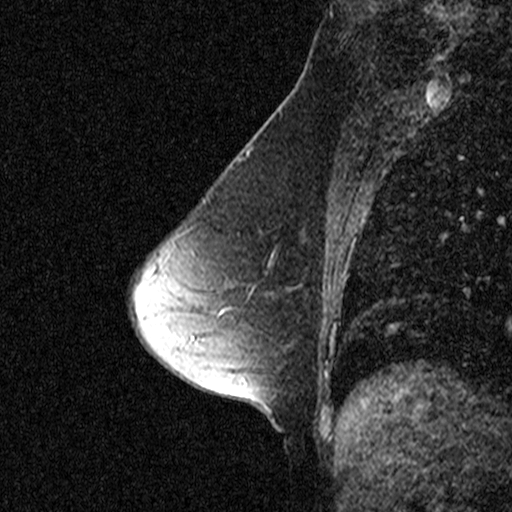
Breast MRI (dynamic contrast-enhanced), one sagittal slice; slice 32 of 44 in the series (ordered by position); dynamic contrast-enhanced study with each time point stored as its own series, time point 2 of 3 at this slice position (early post-contrast, ordered by acquisition time); 1.5 T; TE 4.5 ms, TR 11 ms; 2.27 mm slice thickness; 512 × 512 image matrix, field of view 200 × 200 mm. Patient: female, 53 years. Case-level facts recorded for this patient, not image findings: setting: breast cancer imaged before/during neoadjuvant chemotherapy; receptor status: HR-positive, HER2-negative.
Structures marked on this image (semi-automatically segmented with operator editing):
- analysis volume of interest (the breast-tissue region the enhancement analysis was run in; not a lesion): bounding box <200,178,317,309> (left, top, right, bottom; pixels)
- tumour enhancement mask (voxels above the 90 % enhancement threshold inside the analysis volume of interest): <228,288,253,309>